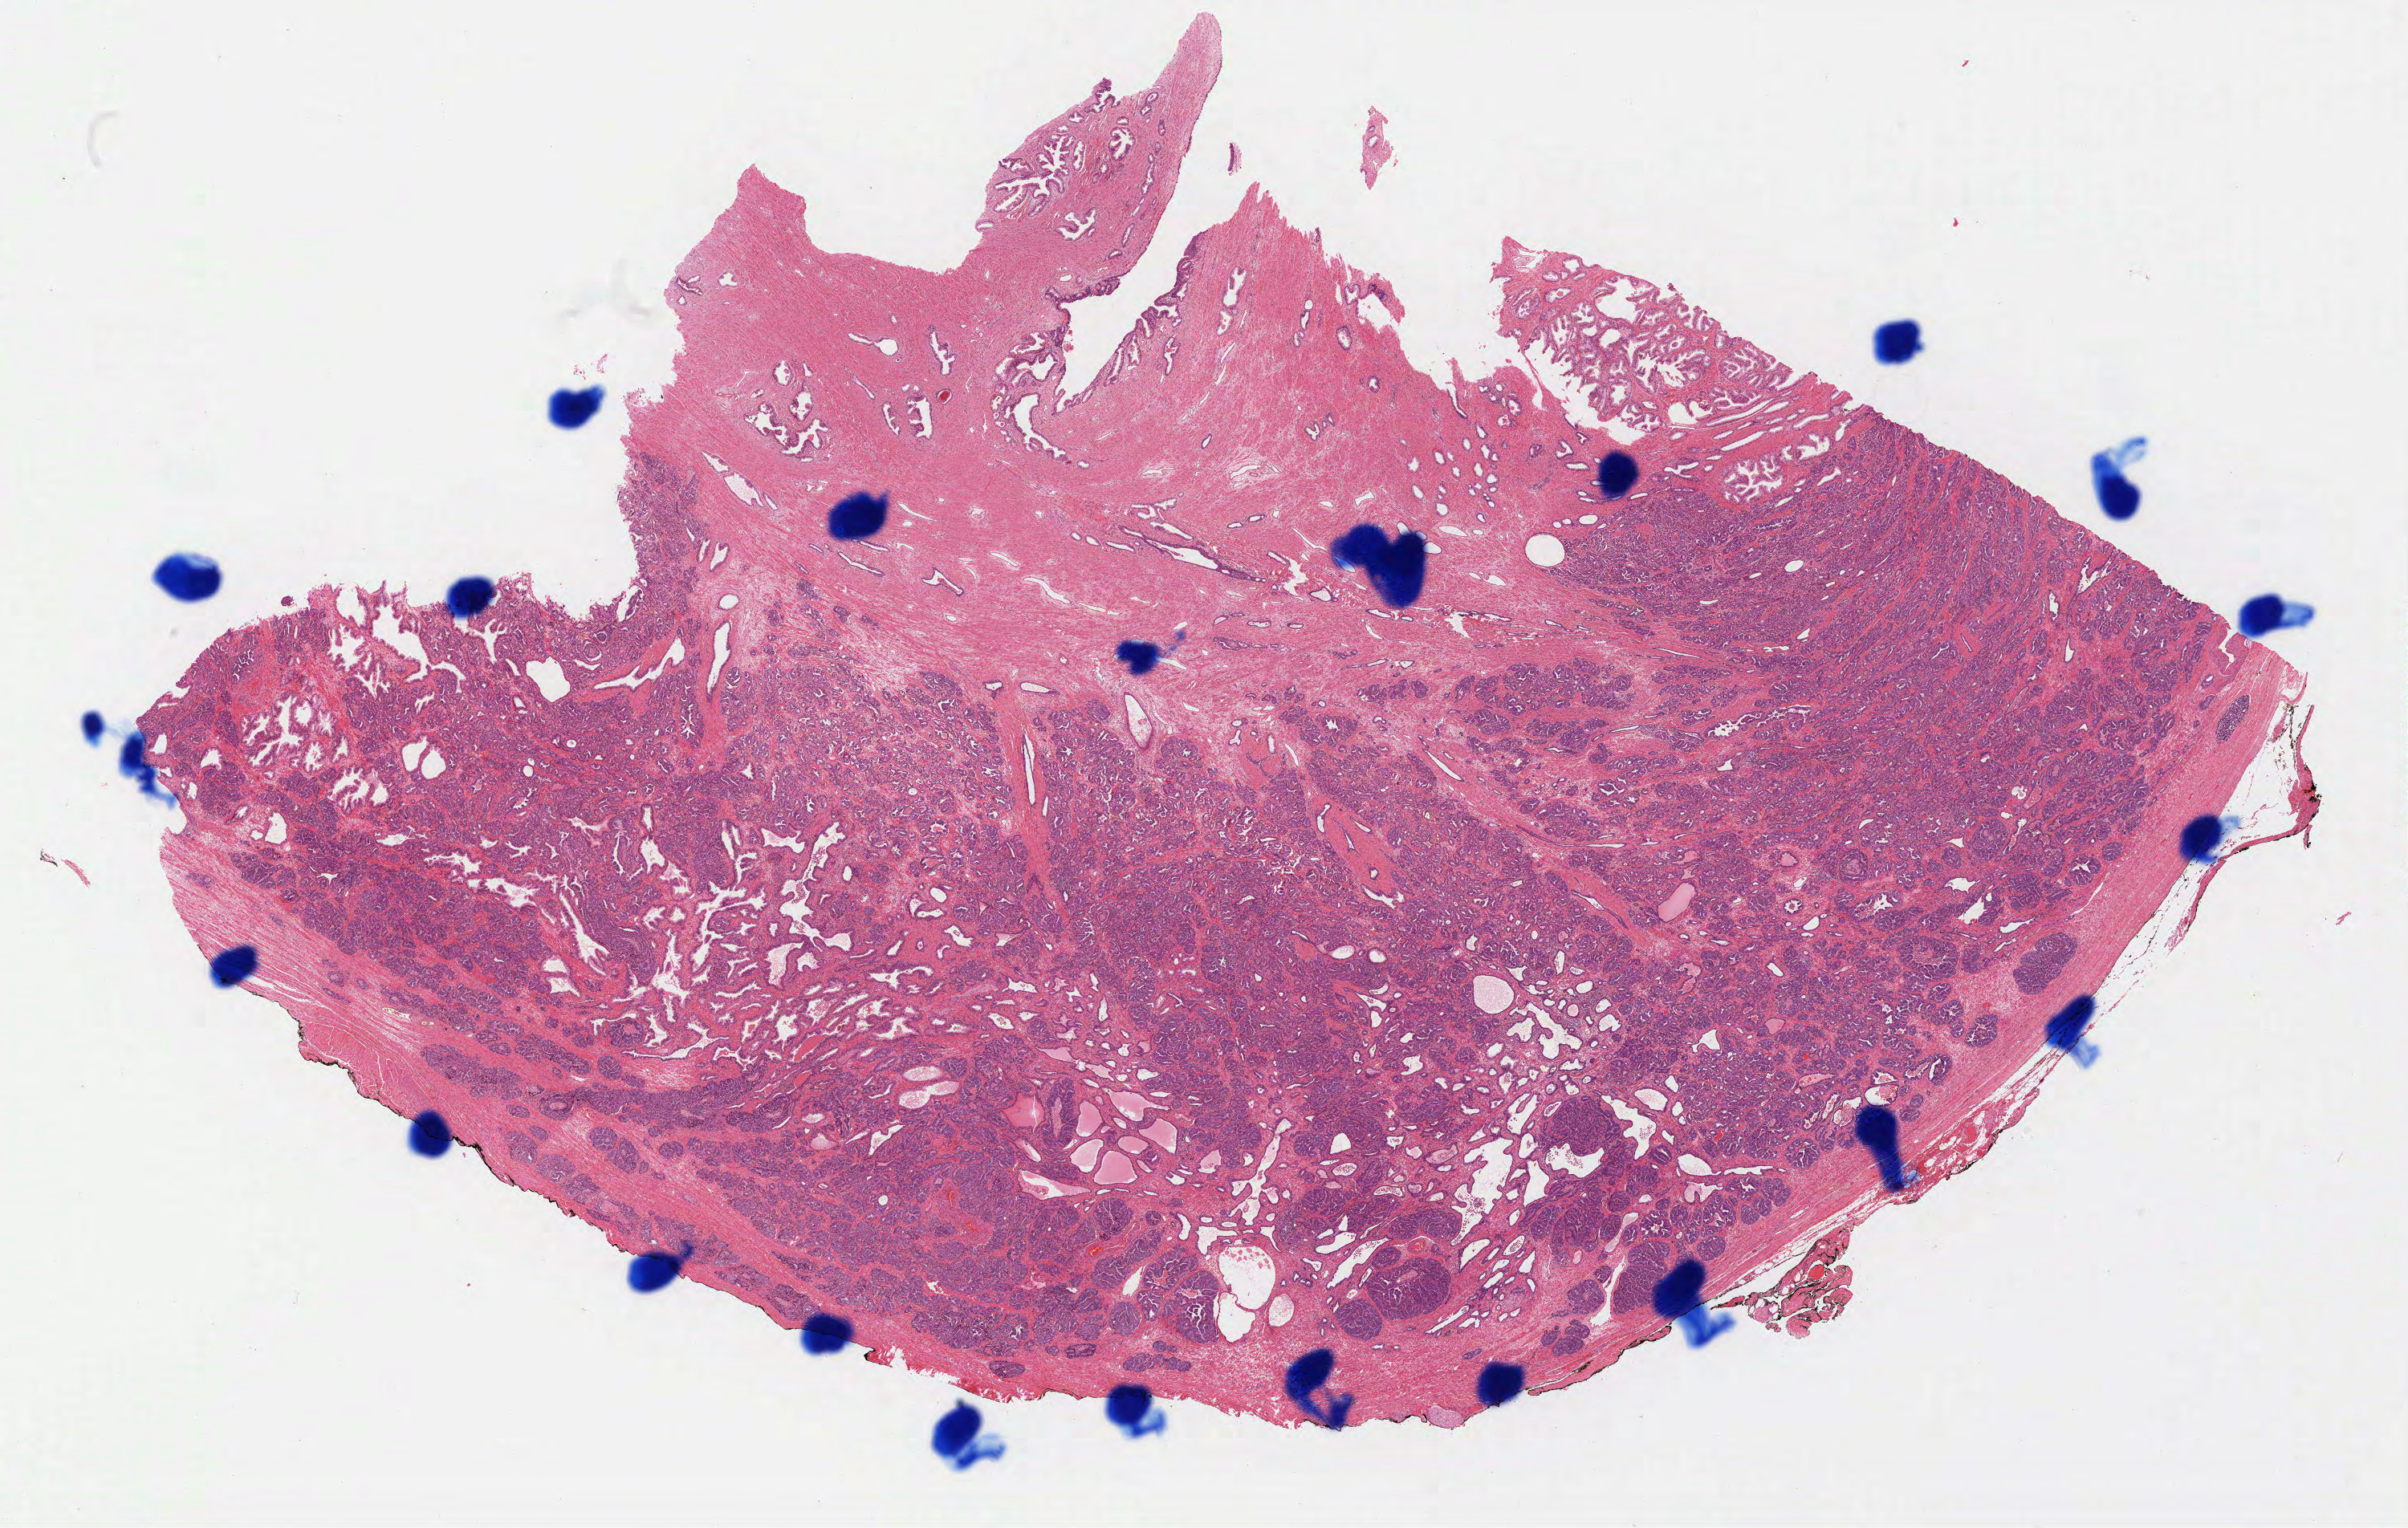
Whole-slide histology image, H&E-stained, shown as a low-resolution overview of the whole scanned area (about 24.0 x 15.2 mm). Formalin-fixed paraffin-embedded (FFPE) diagnostic section. Primary tumour sample from the prostate. Male, age 63 years at initial diagnosis. Gleason score: 8 (4+4).
• pathologic diagnosis: Infiltrating duct carcinoma, NOS (prostate gland)
• laterality: bilateral